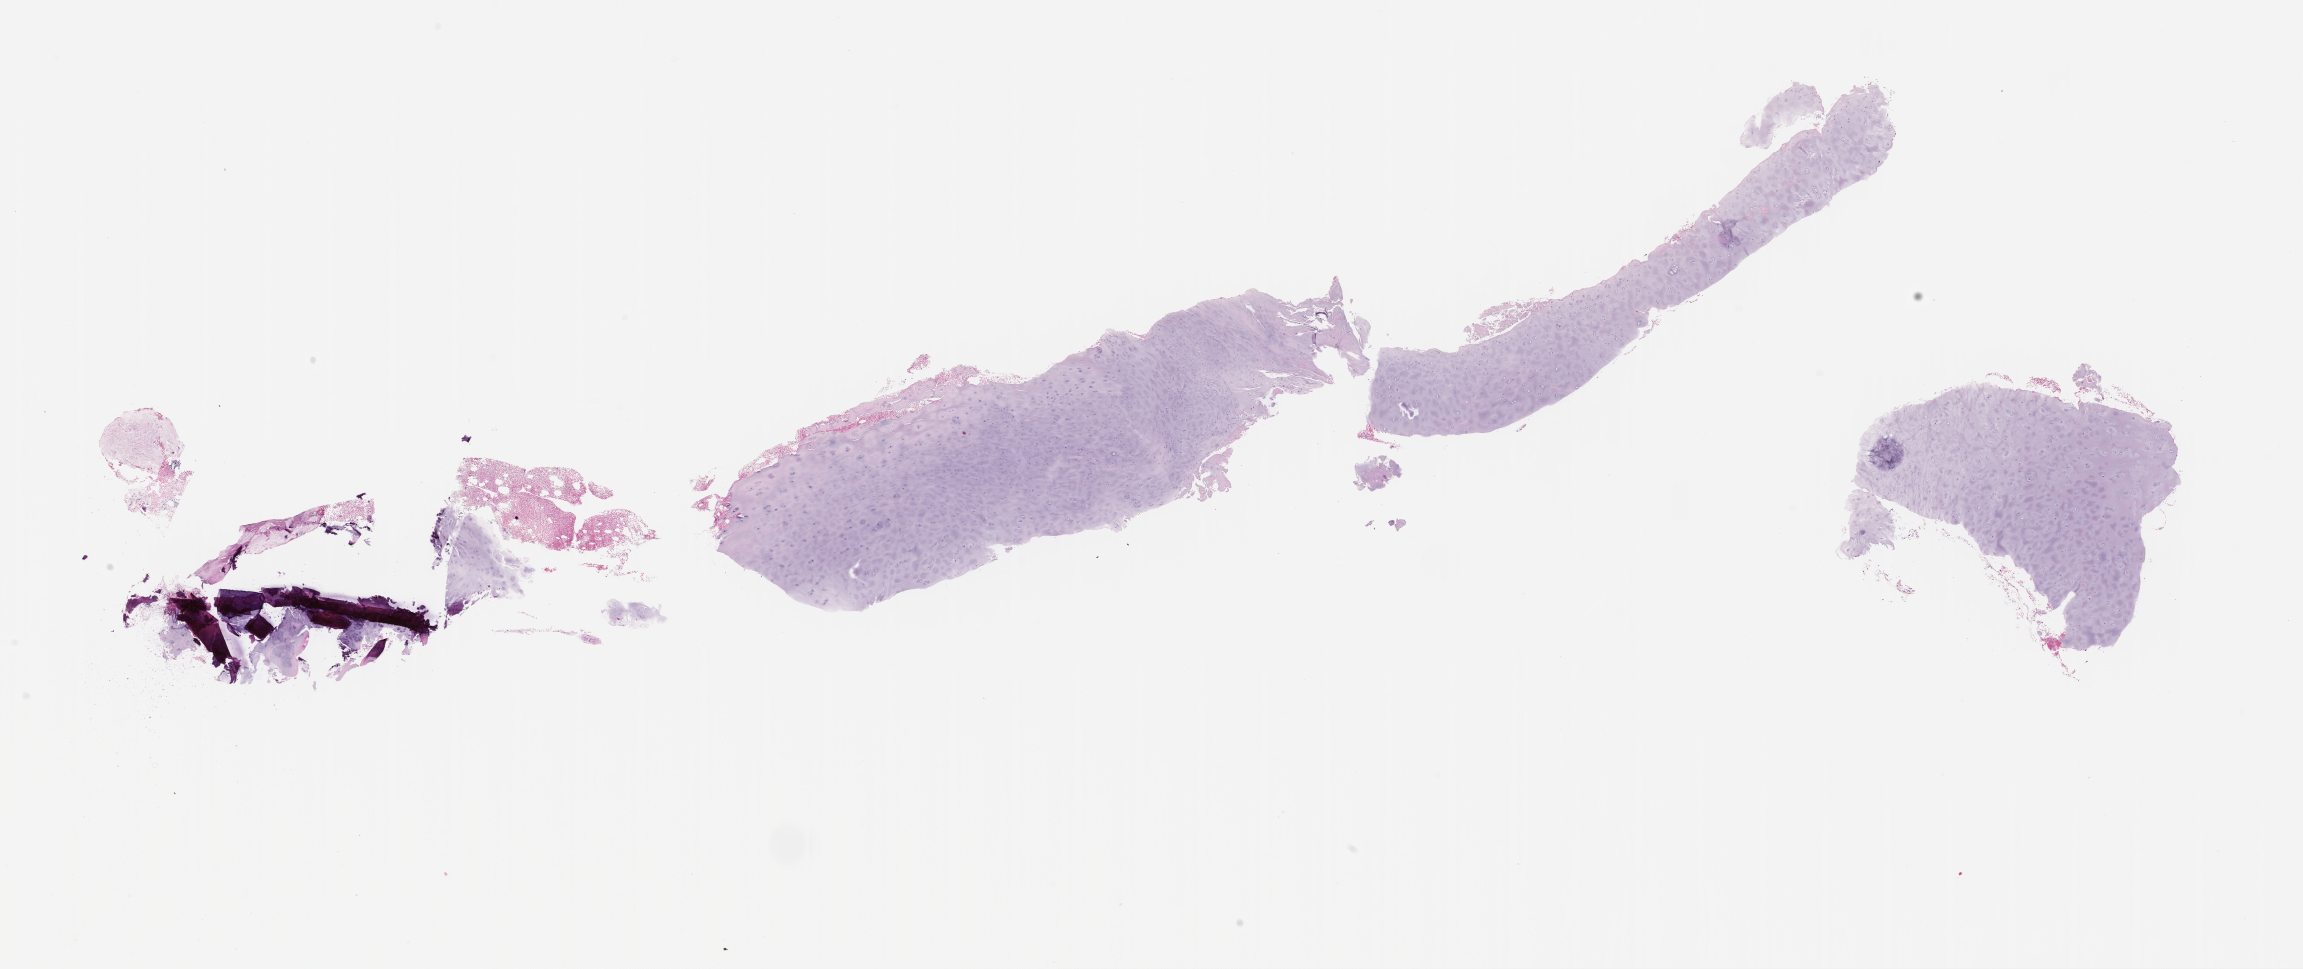
Haematoxylin and eosin whole-slide image, low-resolution overview of the scanned area, about 18.6 x 7.8 mm; formalin-fixed paraffin-embedded section; site: bone marrow; specimen time point: collected at baseline (before treatment). Patient sex: female.
This section: primary tumor. Diagnosis: Plasma Cell Myeloma.